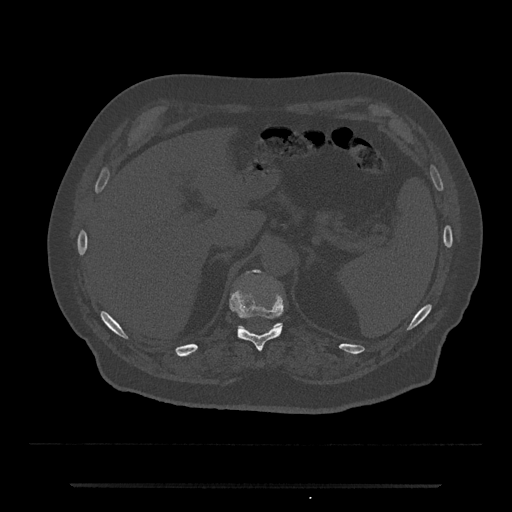
CT including the spine, one axial slice. Slice 639 of 797 in the series (ordered by position). Reconstruction kernel Br40s/3. Bone window (W 1800 / L 400 HU). 0.5 mm slice thickness. 512 × 512 image matrix. Male patient, age 80 years. Case-level facts recorded for this patient, not image findings: primary cancer: prostate.
Structures marked on this image (semi-automatically segmented with operator editing):
- T11 vertebra: bounding box (x1, y1, x2, y2) in pixels: (230, 292, 284, 352)
- T12 vertebra: (237, 269, 282, 332)